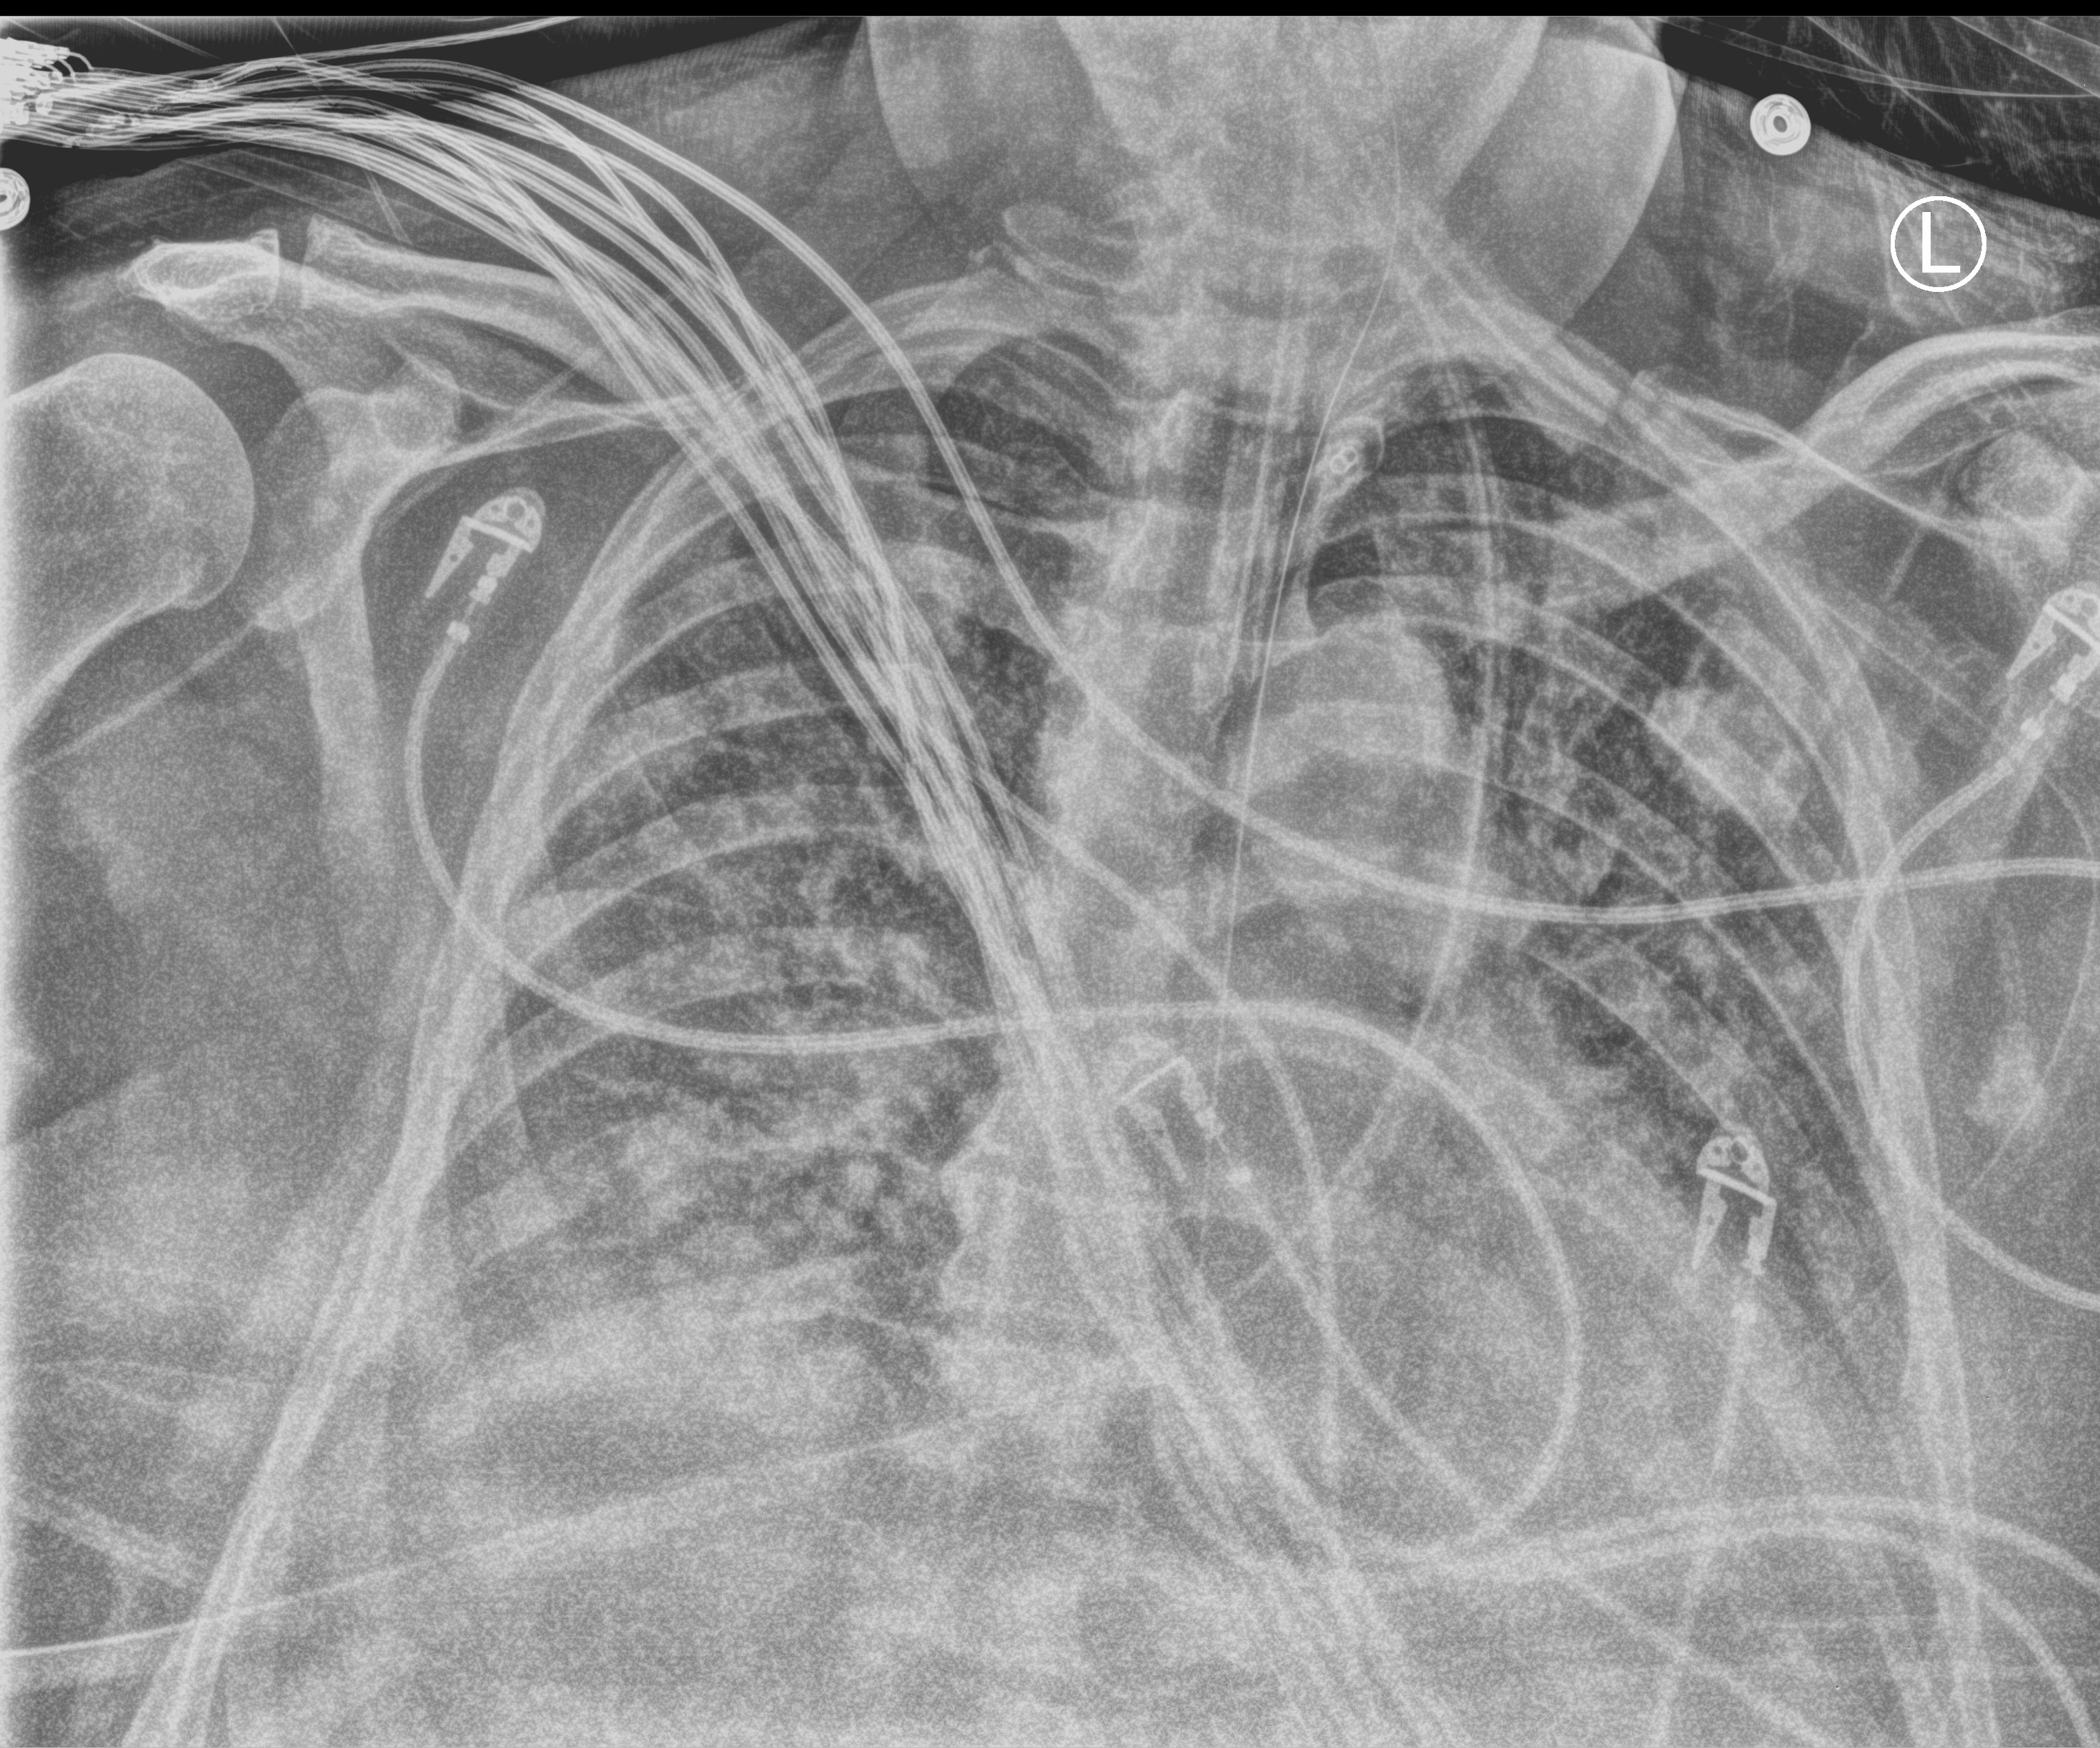
Bedside chest radiograph (computed radiography); anteroposterior (AP) projection. Patient hospitalised with COVID-19; male, aged 60–74 years.
From the hospital-stay record, not from the radiograph (when in the stay this image was taken is not recorded):
- hypertension (admission record): yes
- length of hospital stay: 40 days